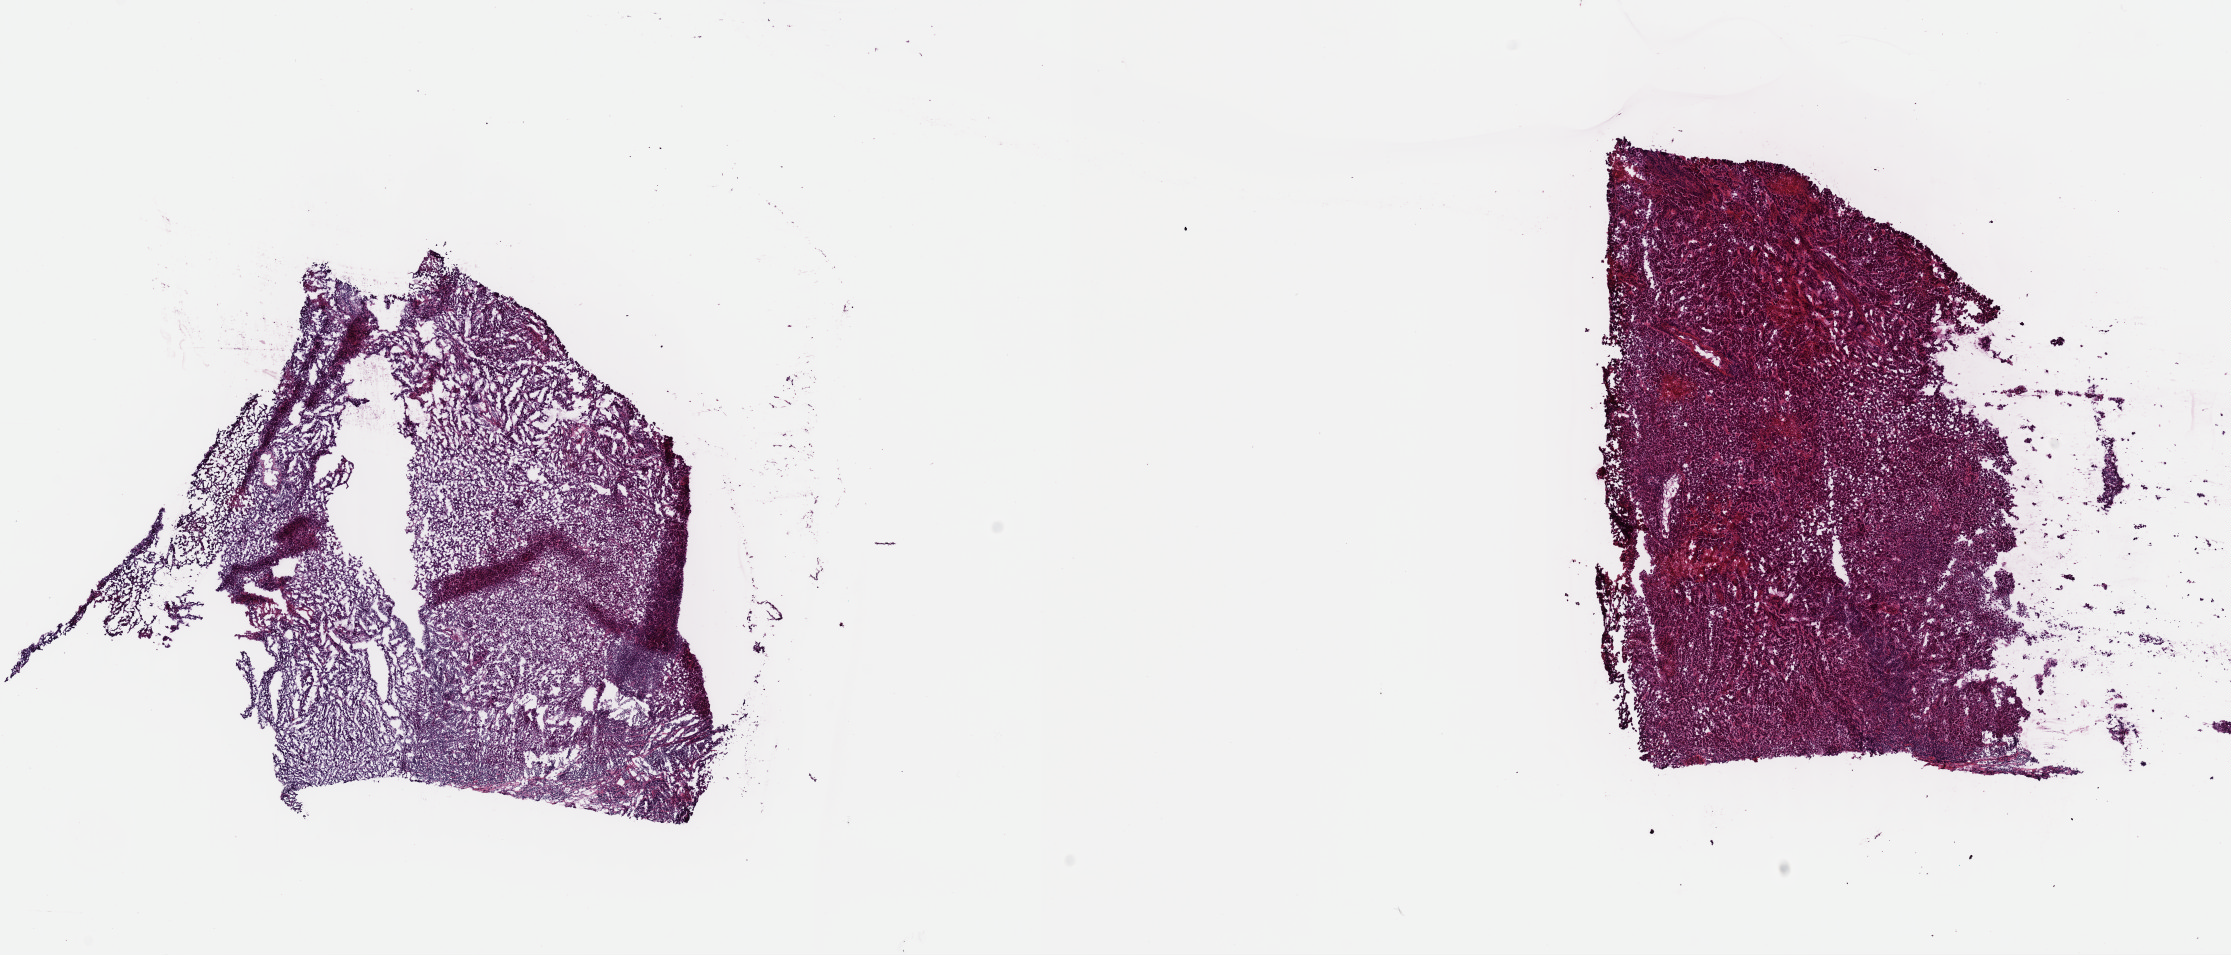
H&E whole-slide image, low-resolution overview of the scanned area, about 17.6 x 7.5 mm. Frozen section. Metastatic tumour sample, sampled site: lymph nodes of axilla or arm. Patient: male, age at initial diagnosis 47 years. Composition of this section per pathologist review: tumour cells 100%, tumour nuclei 95%, normal cells 0%, stromal cells 0%, necrosis 0%. Infiltration values recorded for this section: lymphocyte infiltration 0%, monocyte infiltration 0%, neutrophil infiltration 0%.
This section: metastatic tumour tissue. Patient diagnosis: Malignant melanoma, NOS.